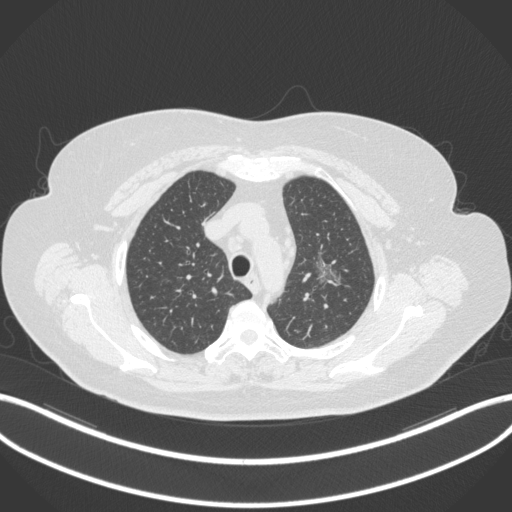
Chest CT, one axial slice. Slice 262 of 310 in the series (ordered by position). 120 kVp. Lung window (W 1500 / L -600 HU). 1 mm slice thickness. 512 × 512 image matrix, field of view 400 × 400 mm. Female patient, age 70 years. From the clinical record (not read from this slice): clinical TNM (as recorded): T1c N0 M0.
Outlined on this slice (bounding box drawn by a radiologist):
- lung tumour (recorded histology: adenocarcinoma): bounding box (x1, y1, x2, y2) in pixels: (308, 246, 346, 295)